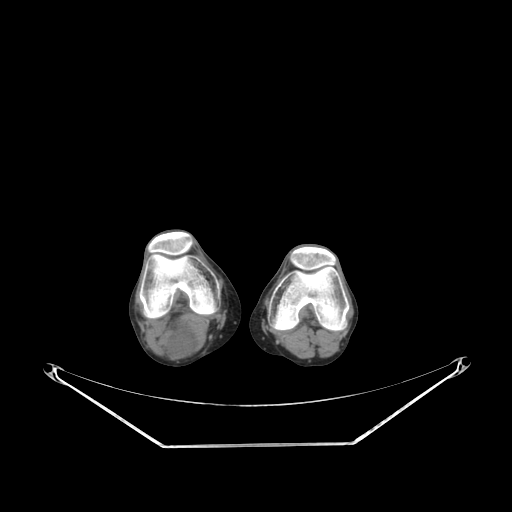
CT of an extremity soft-tissue mass (from a PET/CT study), one axial slice. Position 164 of 267 along the scan axis. Reconstruction kernel SOFT. 140 kVp. Soft-tissue window (W 400 / L 40 HU). 512 × 512 image matrix, field of view 500 × 500 mm. Female patient. From the clinical record (not read from this slice): histological type: liposarcoma; site of the primary tumour: right thigh.
Outlined on this slice (expert contour drawn on MRI and transferred to this co-registered scan by the dataset authors):
- gross tumour volume (mass): bounding box [x1, y1, x2, y2] px = [158, 327, 197, 357]